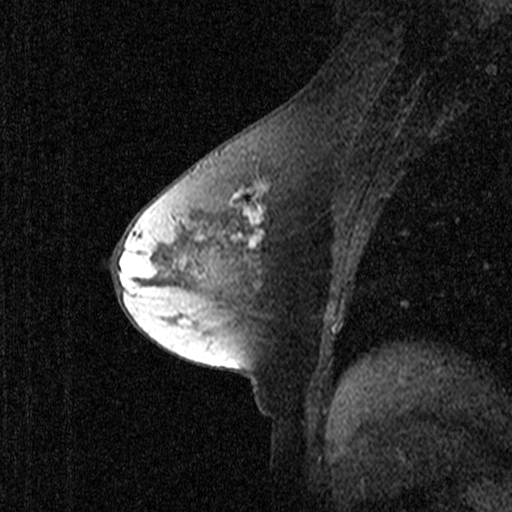
Breast MRI (dynamic contrast-enhanced), one sagittal slice; position 24 of 44 along the scan axis; dynamic contrast-enhanced study with each time point stored as its own series, time point 2 of 3 at this slice position (early post-contrast, ordered by acquisition time); 1.5 T; TE 4.5 ms, TR 11 ms; 2.27 mm slice thickness; 512 × 512 image matrix, field of view 200 × 200 mm. Patient: female, 53 years. From the clinical record (not read from this slice): setting: breast cancer imaged before/during neoadjuvant chemotherapy; receptor status: HR-positive, HER2-negative.
Outlined on this slice (semi-automatically segmented with operator editing):
- analysis volume of interest (the breast-tissue region the enhancement analysis was run in; not a lesion): bounding box (x1, y1, x2, y2) in pixels: (192, 146, 303, 281)
- tumour enhancement mask (voxels above the 90 % enhancement threshold inside the analysis volume of interest): (232, 184, 266, 246)